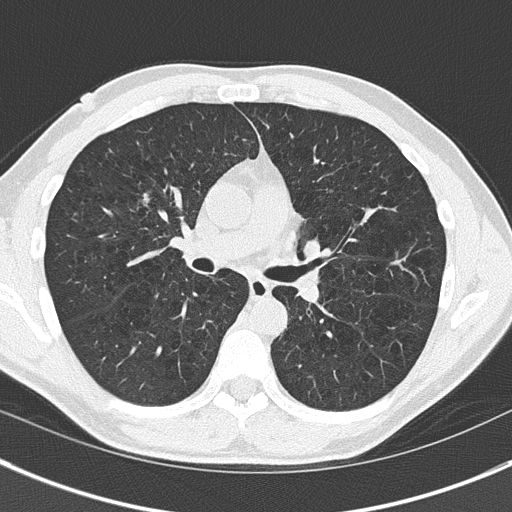
Low-dose screening chest CT, axial slice; baseline annual screen; lung window (W 1500 / L -600 HU); lung (sharp) reconstruction kernel (B50f); slice 78 of 175 in the series; 512 × 512 image matrix. Male participant, aged 56 years at enrolment. Current smoker at enrolment.
Expert-annotated lung lesion, bounding box (x1, y1, x2, y2) in pixels: (128, 184, 162, 217). The screening reader recorded 3 non-calcified nodules or masses ≥4 mm on this exam (right upper lobe, right upper lobe, left lower lobe); which of them this box marks is not recorded. Official screen result: positive, change unspecified: nodule(s) >= 4 mm or enlarging nodule(s), mass(es), or other non-specific abnormalities suspicious for lung cancer.